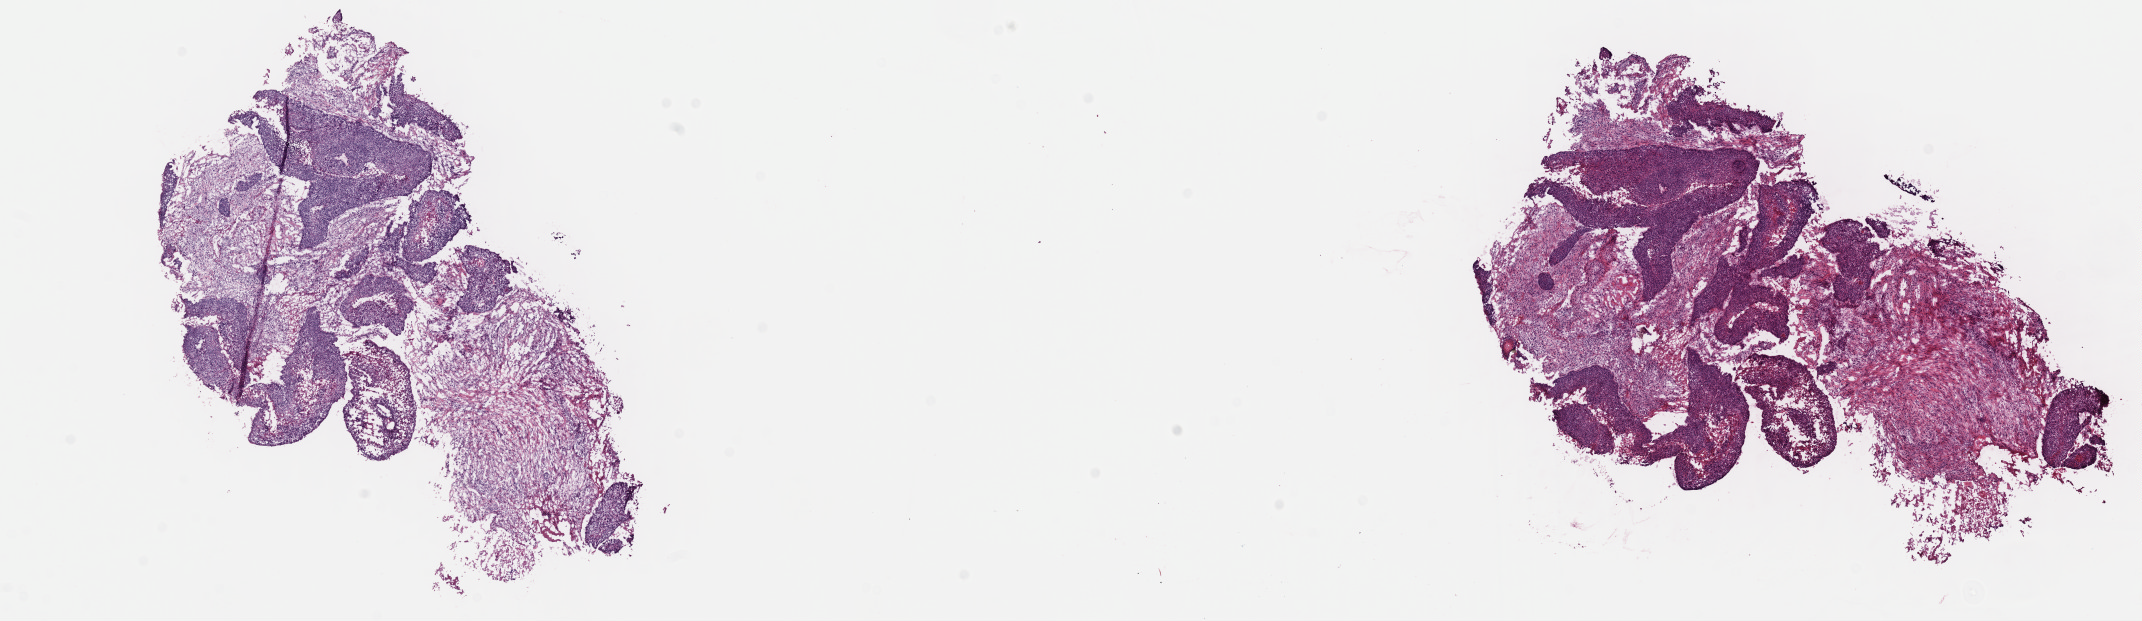
Whole-slide histology image, H&E, shown as a low-resolution overview of the whole scanned area (about 16.9 x 4.9 mm); frozen section from the top of the tissue portion; cervix, primary tumour sample. Female patient; age at initial diagnosis 59 years. Histologic grade: G1 (well differentiated). Slide review estimates, as recorded: tumour cells 50%, tumour nuclei 65%, normal cells 0%, stromal cells 48%, necrosis 2%. Inflammatory infiltration, as recorded: lymphocyte infiltration 5%, monocyte infiltration 1%, neutrophil infiltration 0%.
- FIGO stage: IIB
- diagnosis: Squamous cell carcinoma, large cell, nonkeratinizing, NOS (cervix uteri)